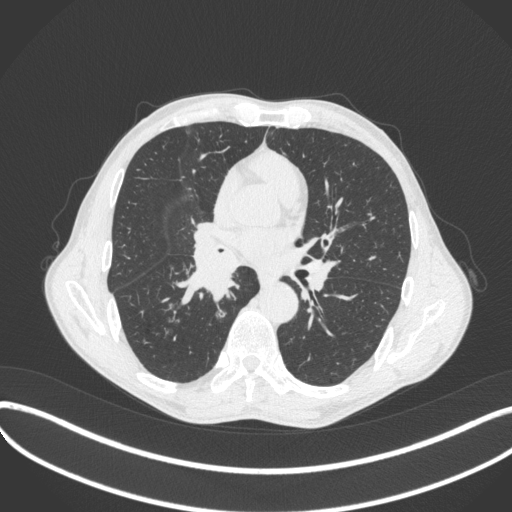
Chest CT, one axial slice; position 227 of 481 along the scan axis; 120 kVp; lung window (W 1500 / L -600 HU); 1 mm slice thickness; 512 × 512 image matrix, field of view 400 × 400 mm. Patient: male, 65 years. From the clinical record (not read from this slice): clinical TNM (as recorded): T2a N0 M0; histopathological grade: G2.
Annotated regions visible in this slice (rectangle marked by the reading radiologist):
- lung tumour (recorded histology: squamous cell carcinoma): bounding box (x1, y1, x2, y2) in pixels: (173, 234, 241, 307)